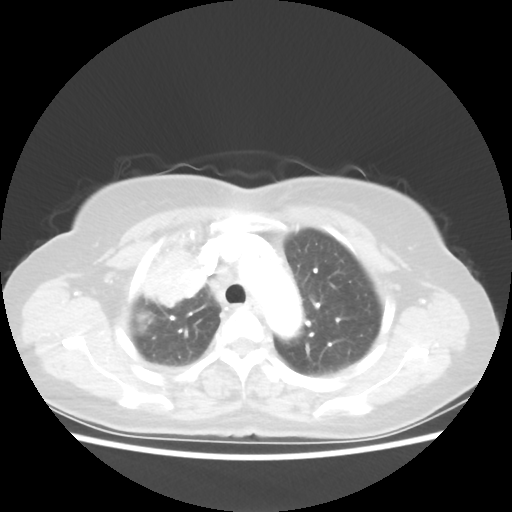
Chest CT, one axial slice; reconstruction kernel STANDARD; 80 kVp; lung window (W 1500 / L -600 HU); 5 mm slice thickness; 512 × 512 image matrix, field of view 337 × 337 mm. Female patient, age 62 years. Case-level facts recorded for this patient, not image findings: clinical TNM (as recorded): T4 N3 M0.
Outlined on this slice (rectangle marked by the reading radiologist):
- lung tumour (recorded histology: squamous cell carcinoma): bounding box <142,239,213,312> (left, top, right, bottom; pixels)